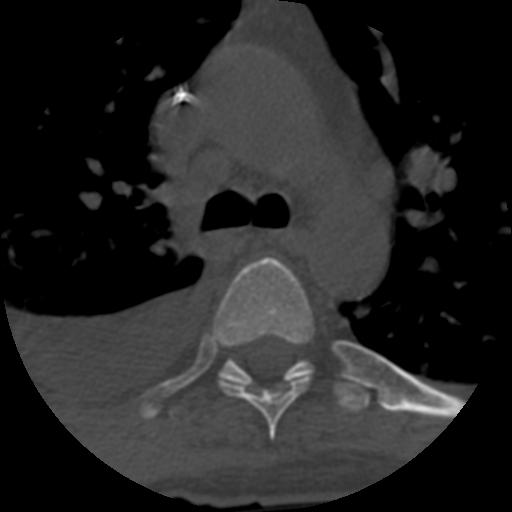
CT including the spine, one axial slice. Reconstruction kernel STANDARD. 120 kVp. One of 3 acquisitions stored at this slice position. Bone window (W 1800 / L 400 HU). 1.25 mm slice thickness. 512 × 512 image matrix, field of view 160 × 160 mm. Patient age 55 years. Case-level facts recorded for this patient, not image findings: primary cancer: colon; vertebrae with lytic lesions (as recorded): T12, L1, L5.
Annotated regions visible in this slice (semi-automatic segmentation, software-assisted and operator-edited):
- T5 vertebra: box from (x=215, y=257) to (x=313, y=440) px
- T6 vertebra: (x=170, y=358)–(x=370, y=416)